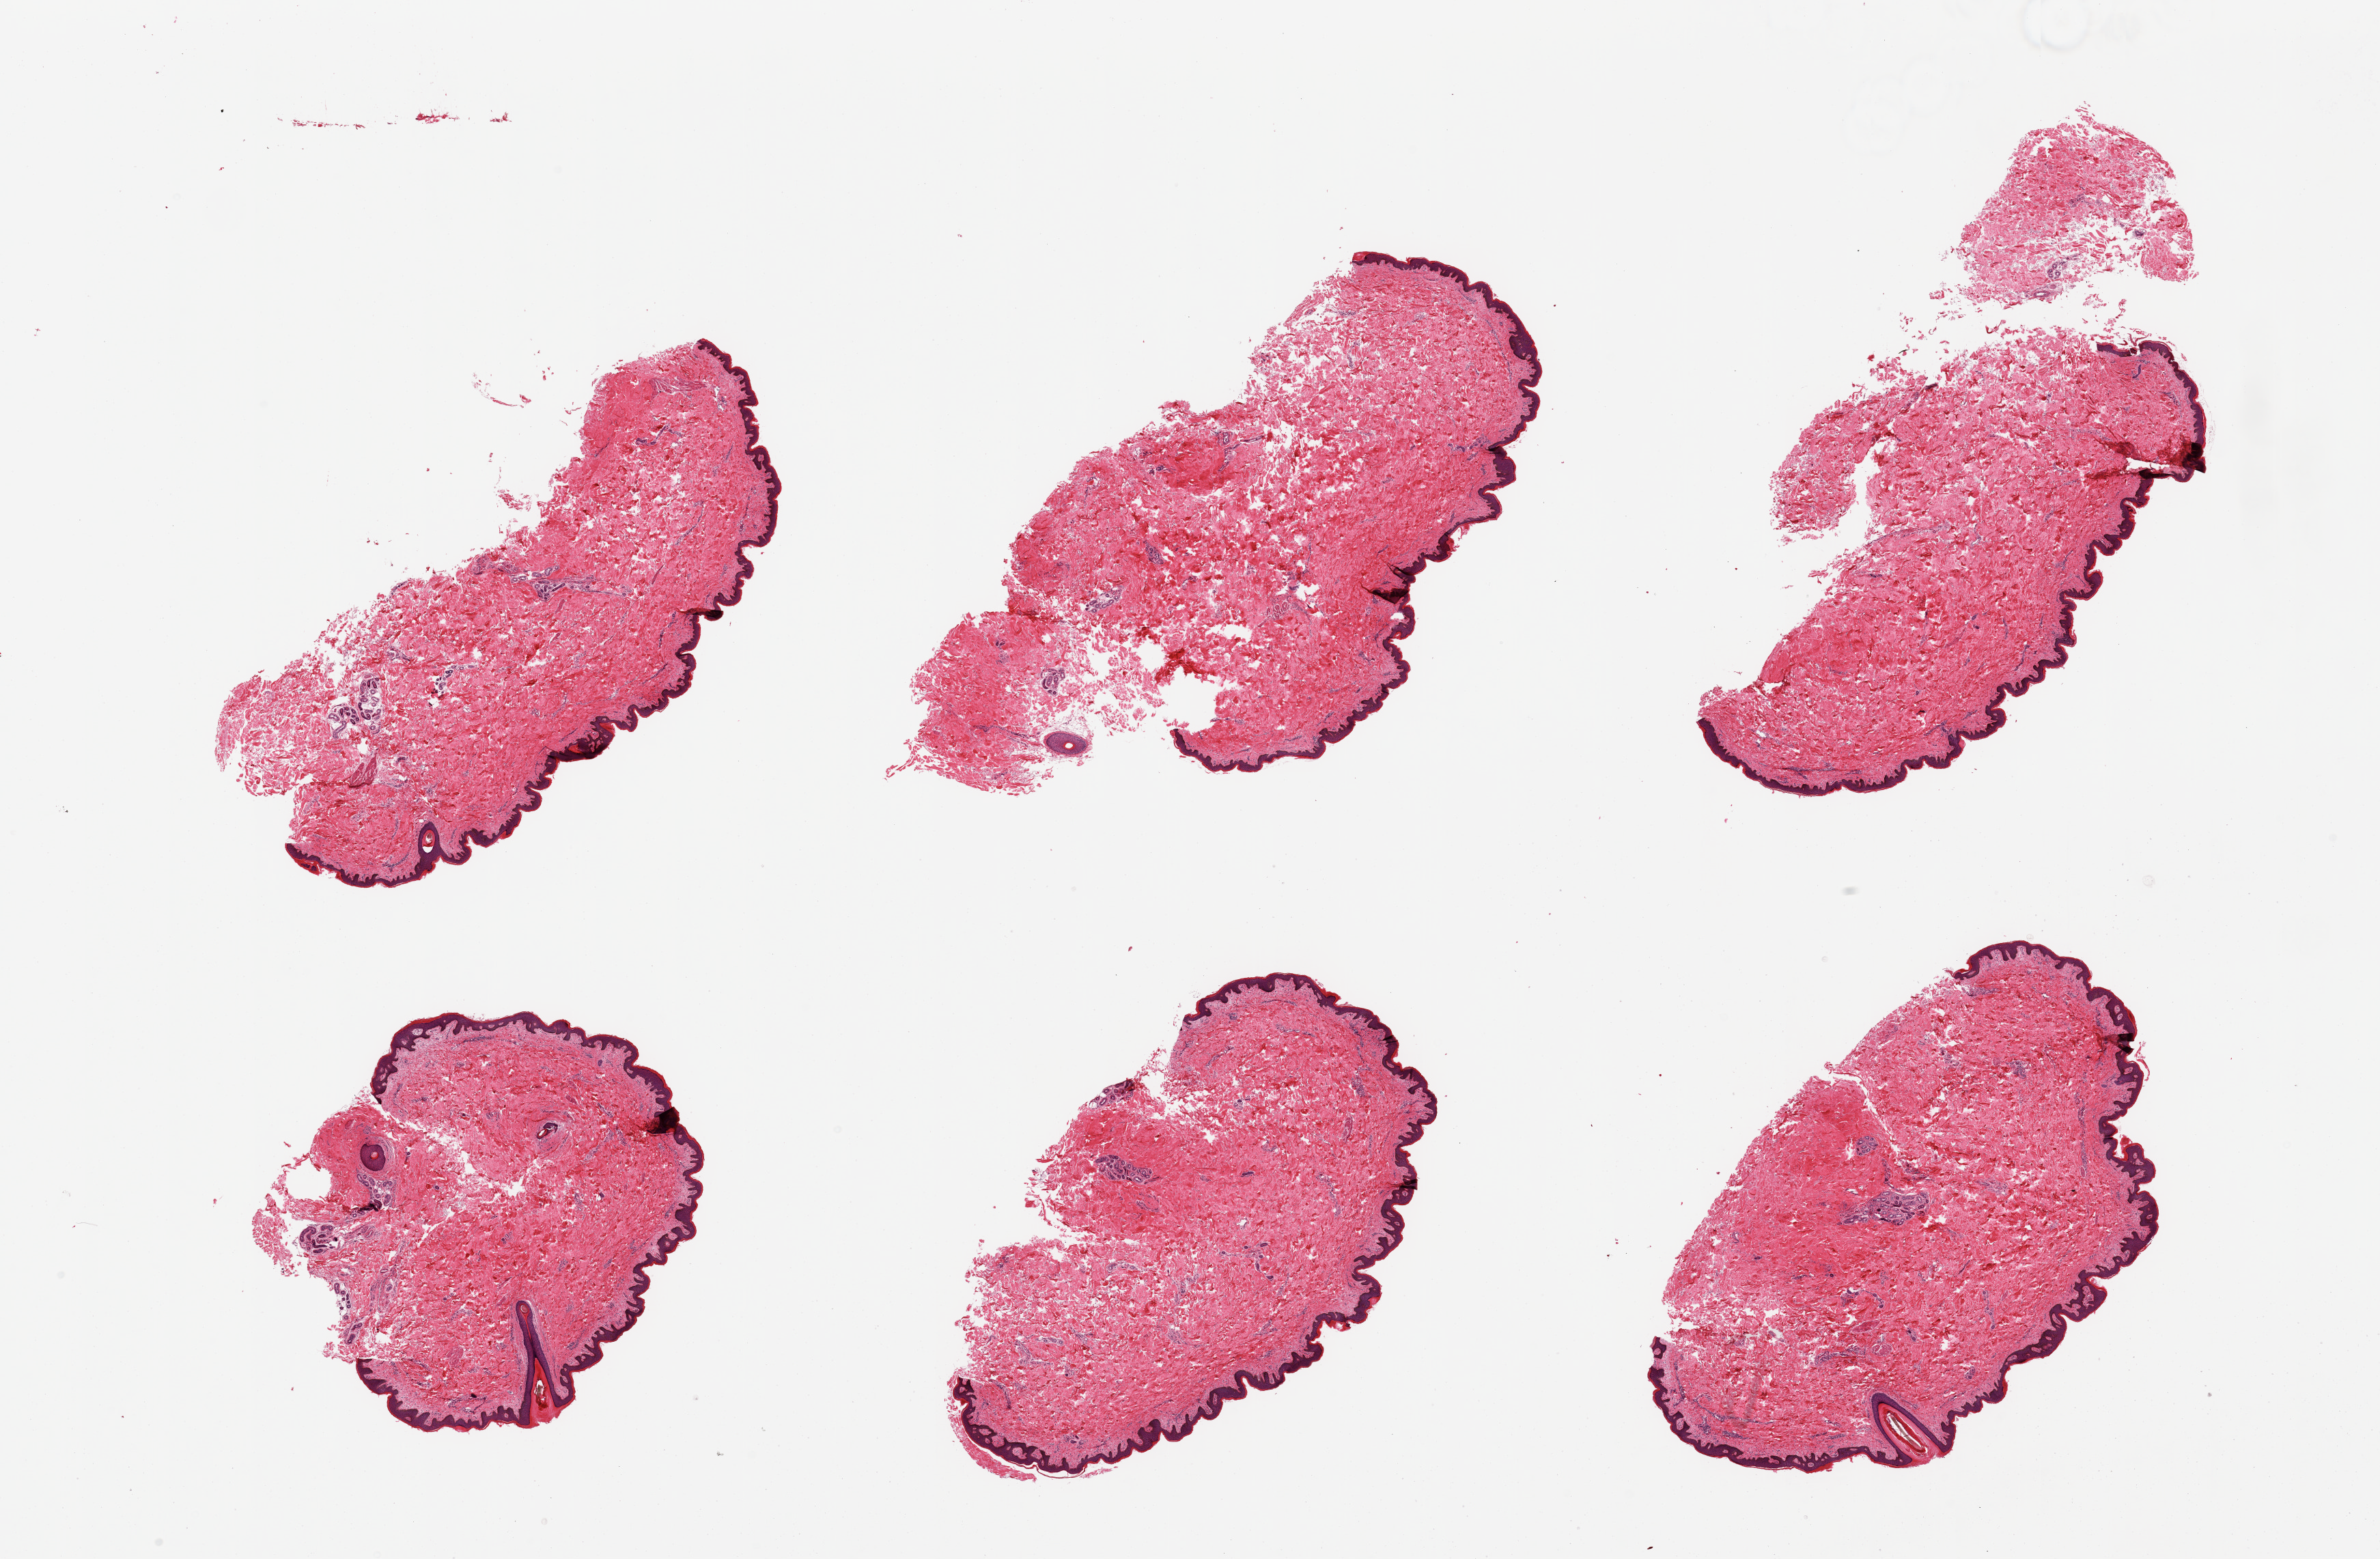
Haematoxylin and eosin whole-slide image, brightfield, shown as a low-resolution overview of the whole scanned area (about 27.6 x 18.1 mm, from a 20x scan); PAXgene-fixed paraffin-embedded (PFPE) section; sampled site (target tissue): skin of suprapubic region; tissue donor sample.
Pathologist's review note for this sample: 6 pieces; minimal internal fat.